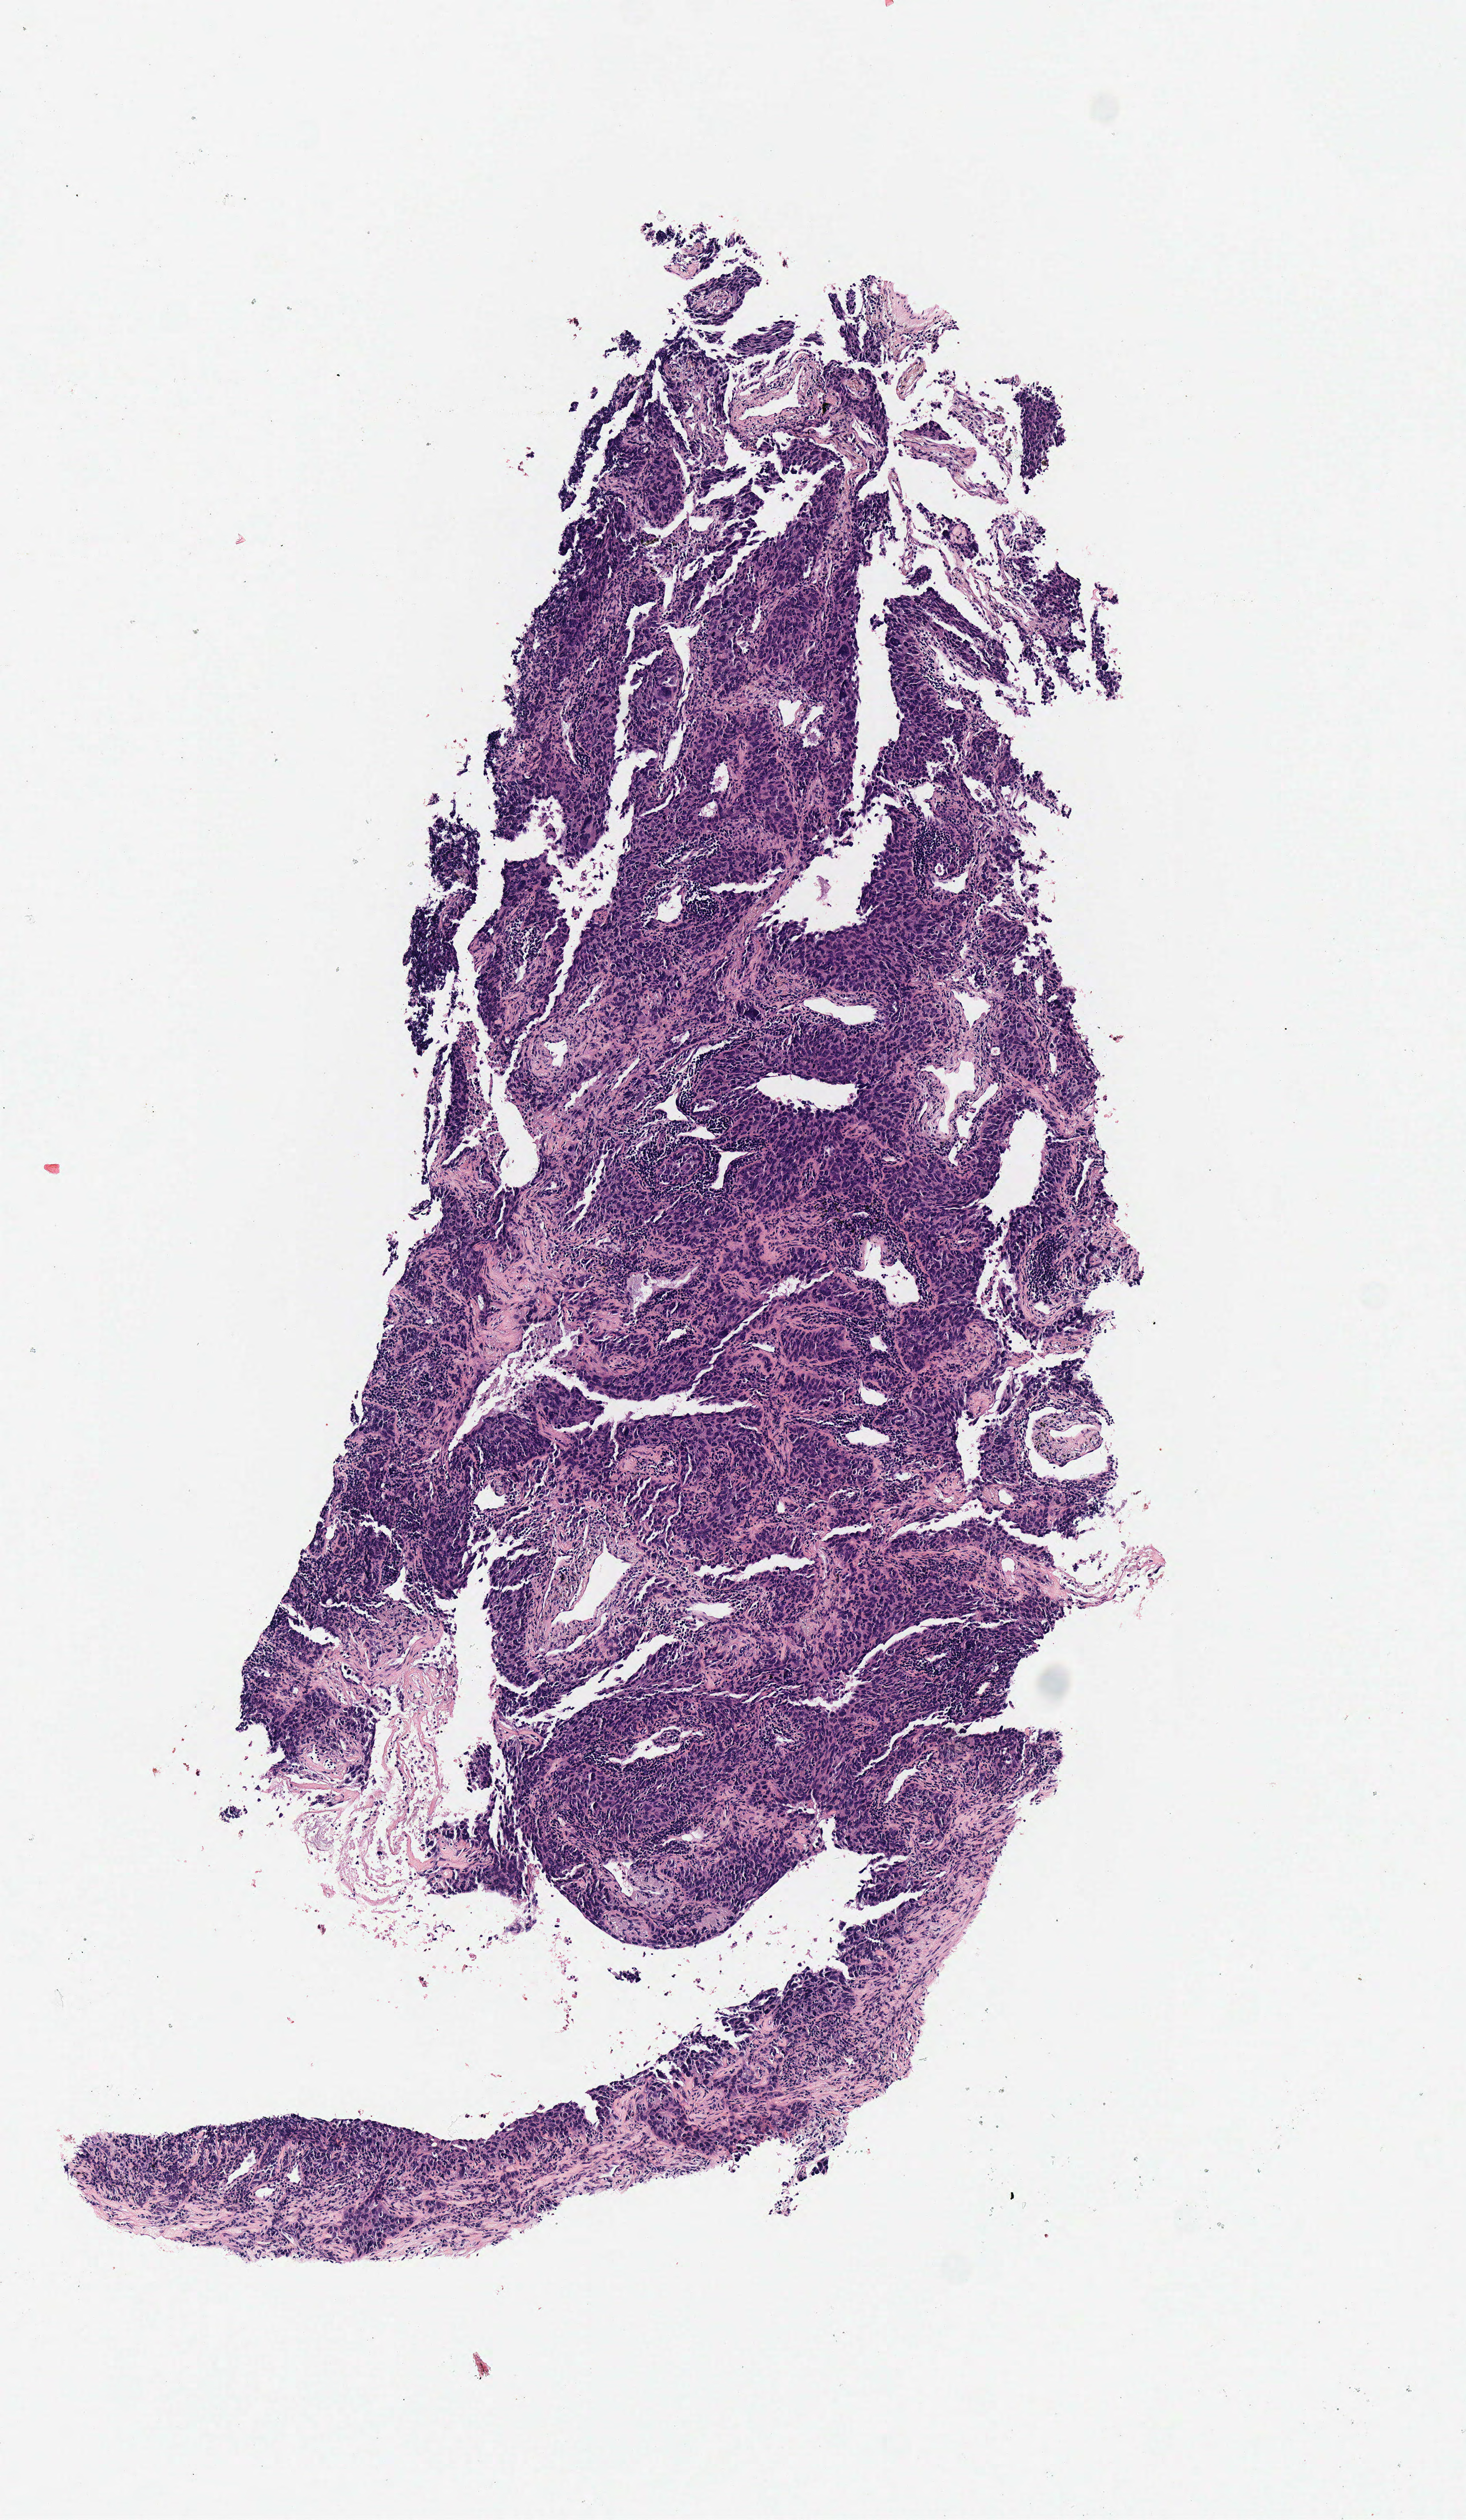
Whole-slide histology image, H&E — low-resolution overview of the scanned area, about 3.5 x 6.0 mm (slide scanned at 40x). Frozen section. Sample: primary tumour, lung. Male patient; age at initial diagnosis 79 years. Composition of this section per pathologist review: tumour cells 95%, tumour nuclei 75%, normal cells 0%, stromal cells 5%, necrosis 0%.
• AJCC pathologic stage: IIB (6th edition)
• histologic diagnosis: Squamous cell carcinoma, NOS (overlapping lesion of lung)
• TNM: T2 N1 M0